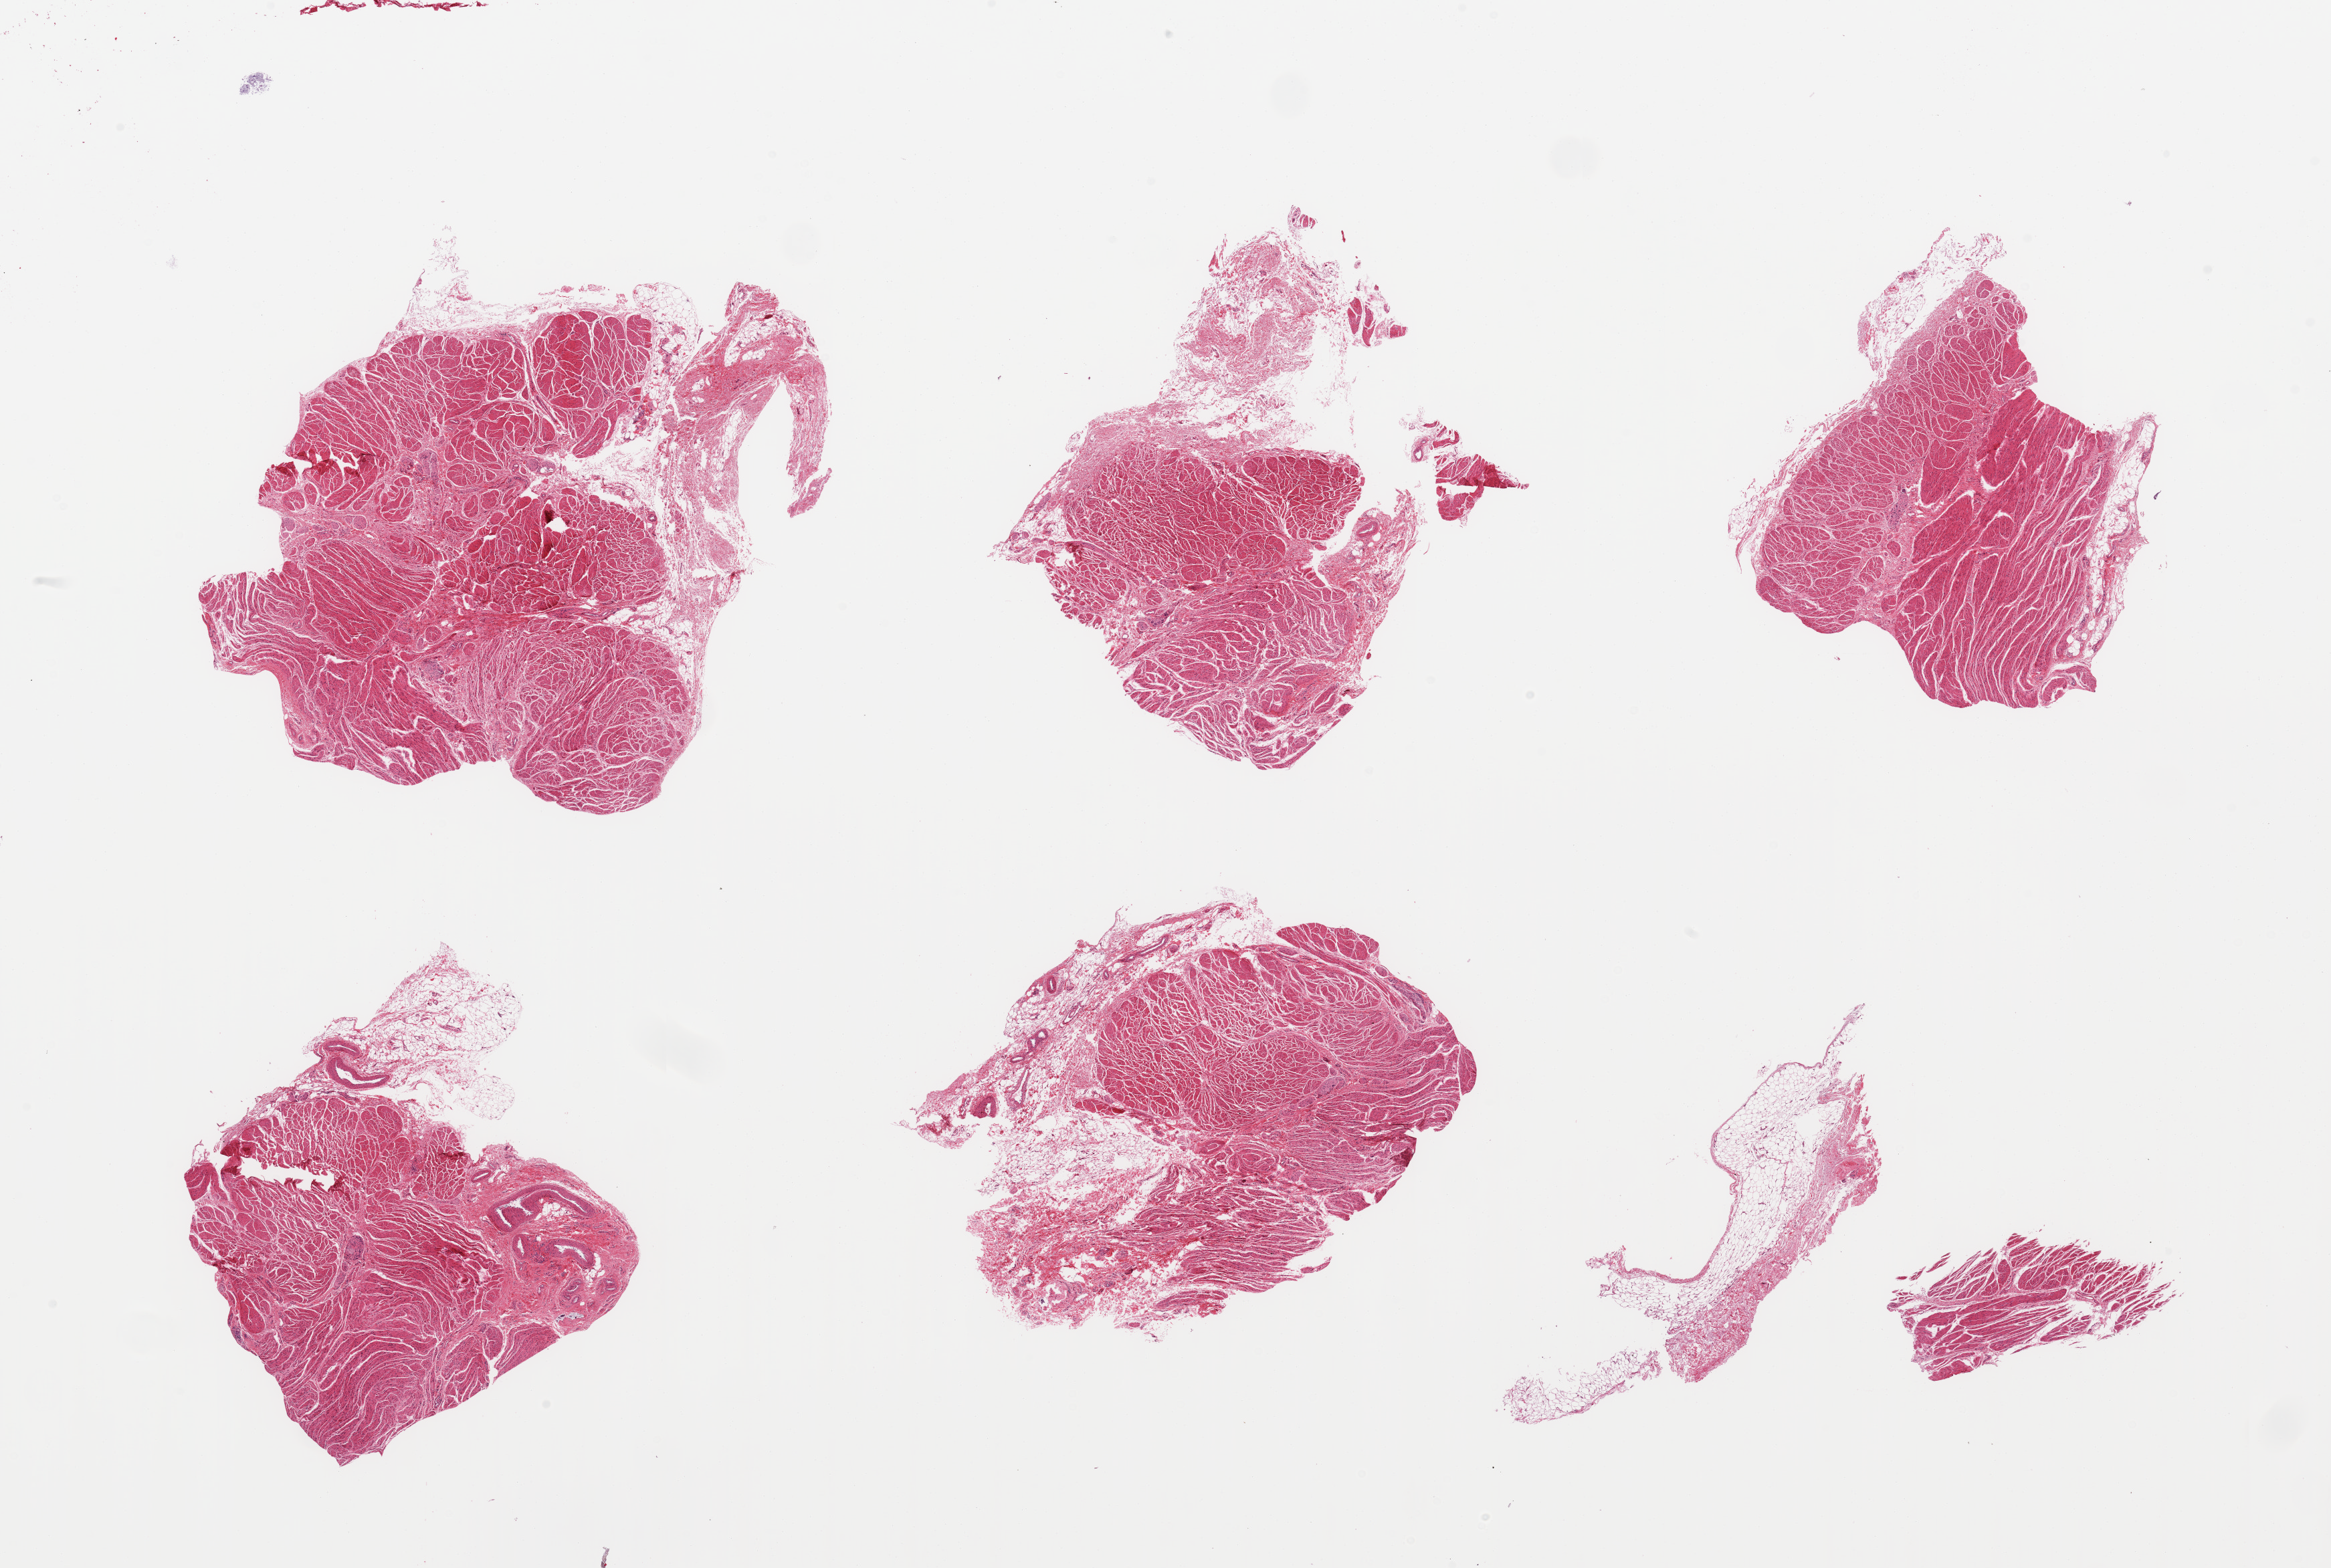
Digitized H&E-stained section, brightfield — a low-resolution overview of the entire scanned area, about 27.6 x 18.5 mm. PAXgene-fixed, paraffin-embedded tissue. Section of gastroesophageal junction (target tissue). Donor tissue sample. Donor: male.
Pathologist's review note for this sample: 6 pieces; variable amounts of fibrofatty external stroma.